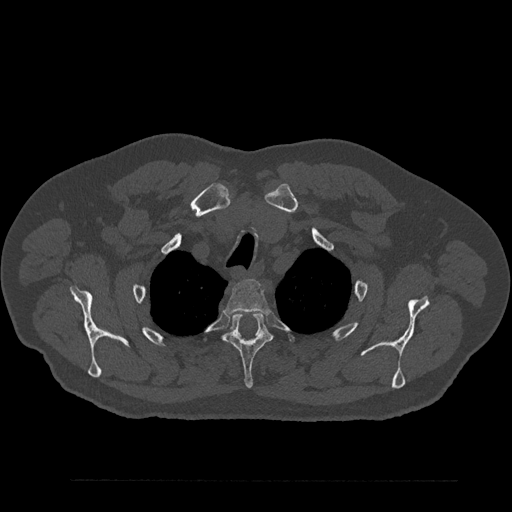
CT including the spine, one axial slice; position 689 of 797 along the scan axis; 120 kVp; bone window (W 1800 / L 400 HU); 0.5 mm slice thickness; 512 × 512 image matrix, field of view 430 × 430 mm. Male patient, age 61 years. From the clinical record (not read from this slice): primary cancer: prostate.
Outlined on this slice (semi-automatic segmentation, software-assisted and operator-edited):
- T2 vertebra: bounding box <224,279,269,314> (left, top, right, bottom; pixels)
- T3 vertebra: <223,313,272,389>